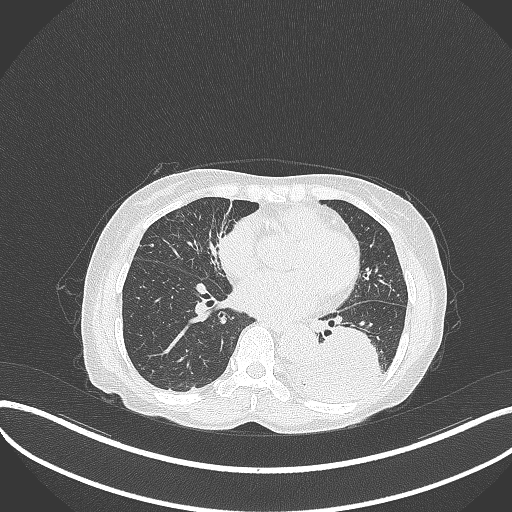
Chest CT, one axial slice. 120 kVp. Lung window (W 1500 / L -600 HU). 1 mm slice thickness. 512 × 512 image matrix, field of view 400 × 400 mm. Female patient, age 78 years. From the clinical record (not read from this slice): clinical TNM (as recorded): T3 N0 M1.
Outlined on this slice (bounding box drawn by a radiologist):
- lung tumour (recorded histology: squamous cell carcinoma): bounding box <294,323,385,400> (left, top, right, bottom; pixels)